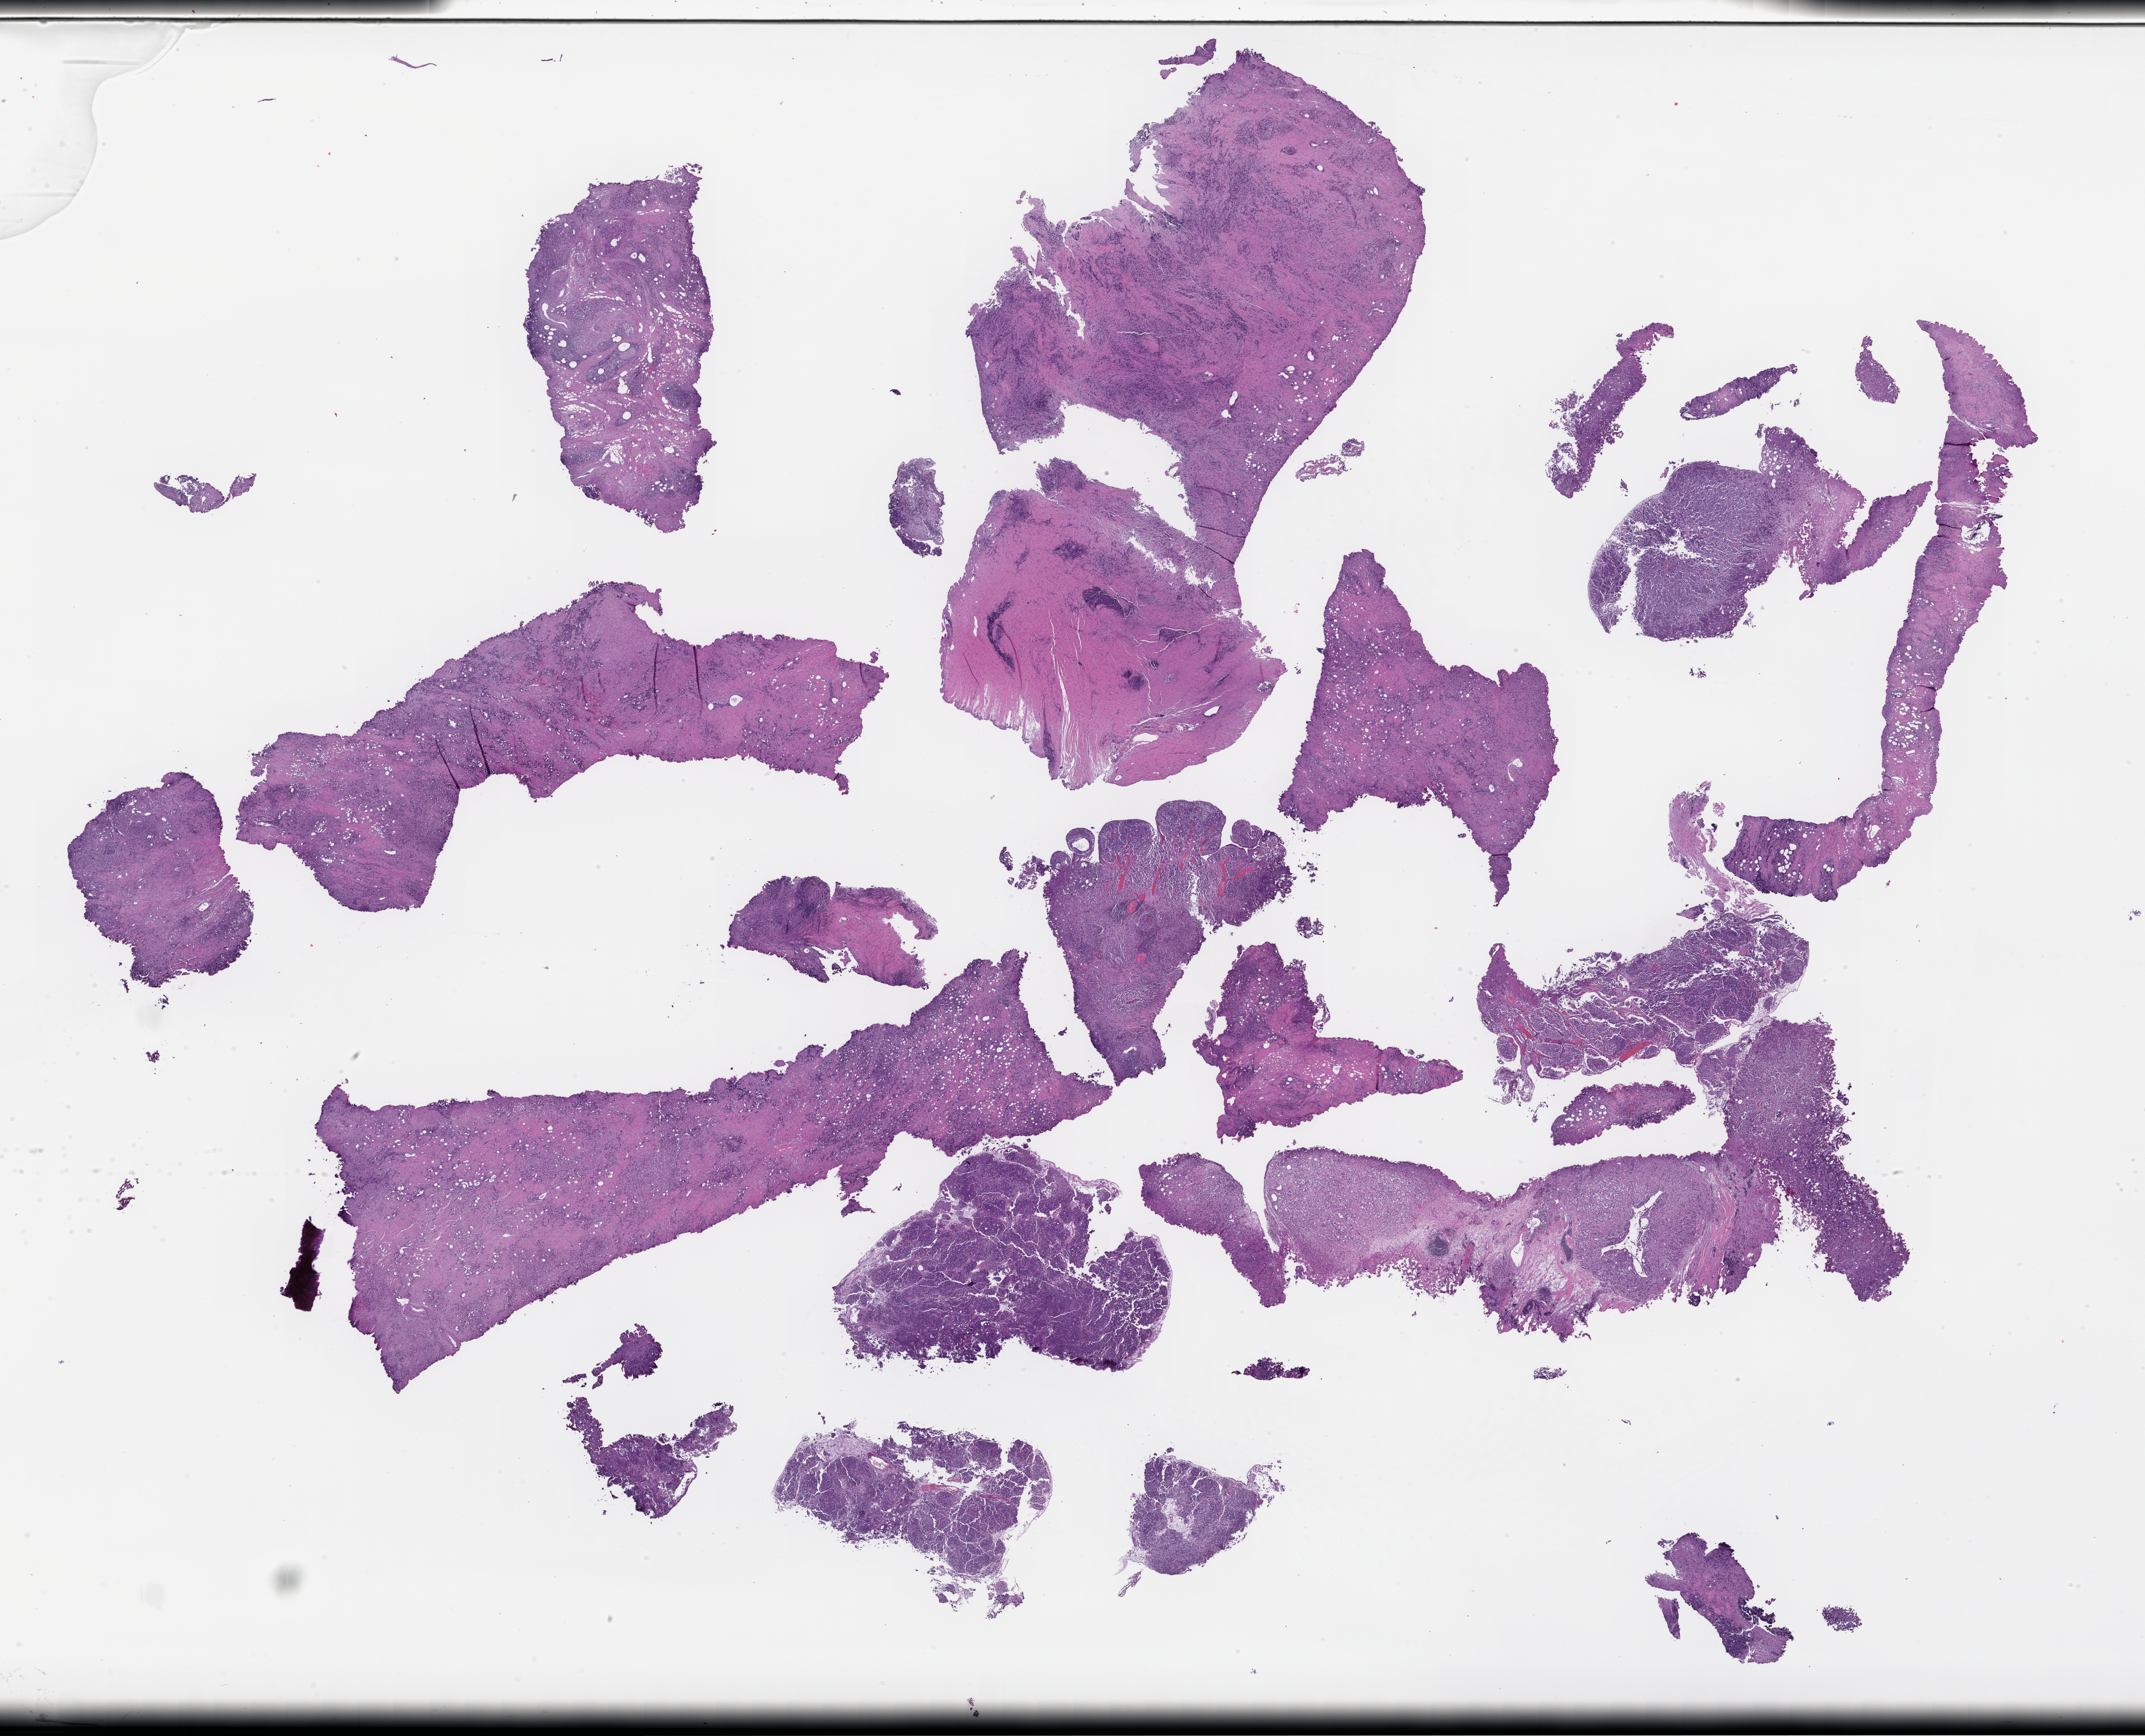
Hematoxylin and eosin (H&E) whole-slide image — low-resolution overview of the scanned area, about 30.2 x 24.4 mm. FFPE section. Tissue site: prostate. Archival tissue. Male patient.
This section: primary tumour tissue. Diagnosis: Prostate Carcinoma.